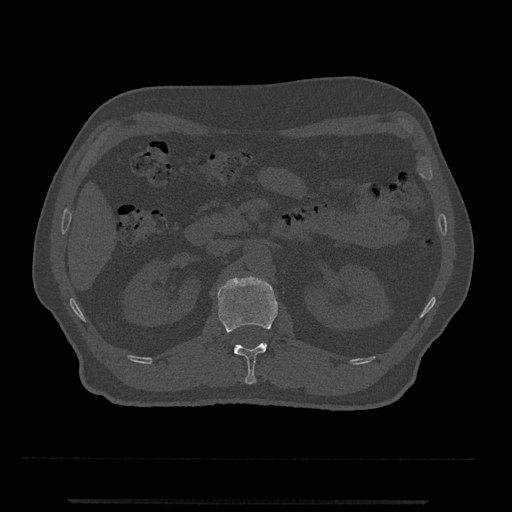
CT including the spine, one axial slice; slice 322 of 797 in the series (ordered by position); 120 kVp; bone window (W 1800 / L 400 HU); 0.5 mm slice thickness; 512 × 512 image matrix, field of view 419 × 419 mm. Patient: male, 63 years. Case-level facts recorded for this patient, not image findings: primary cancer: prostate.
Structures marked on this image (semi-automatically segmented with operator editing):
- L1 vertebra: bounding box (x1, y1, x2, y2) in pixels: (217, 275, 278, 385)